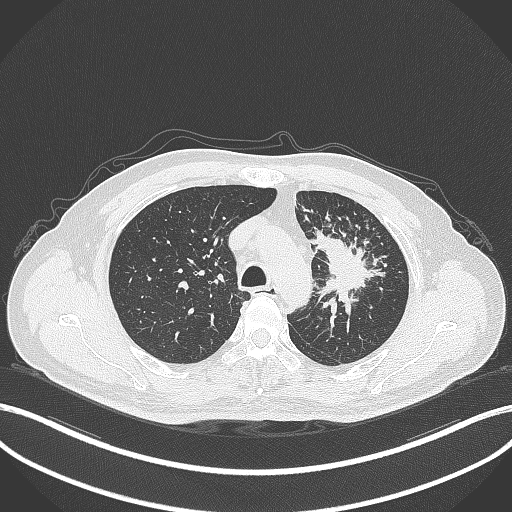
Chest CT, one axial slice; slice 266 of 386 in the series (ordered by position); lung window (W 1500 / L -600 HU); 1 mm slice thickness; 512 × 512 image matrix. Patient: male, 69 years. From the clinical record (not read from this slice): clinical TNM (as recorded): T2a N2 M0; histopathological grade: G2-3.
Structures marked on this image (rectangle marked by the reading radiologist):
- lung tumour (recorded histology: adenocarcinoma): bounding box (x1, y1, x2, y2) in pixels: (308, 225, 389, 316)